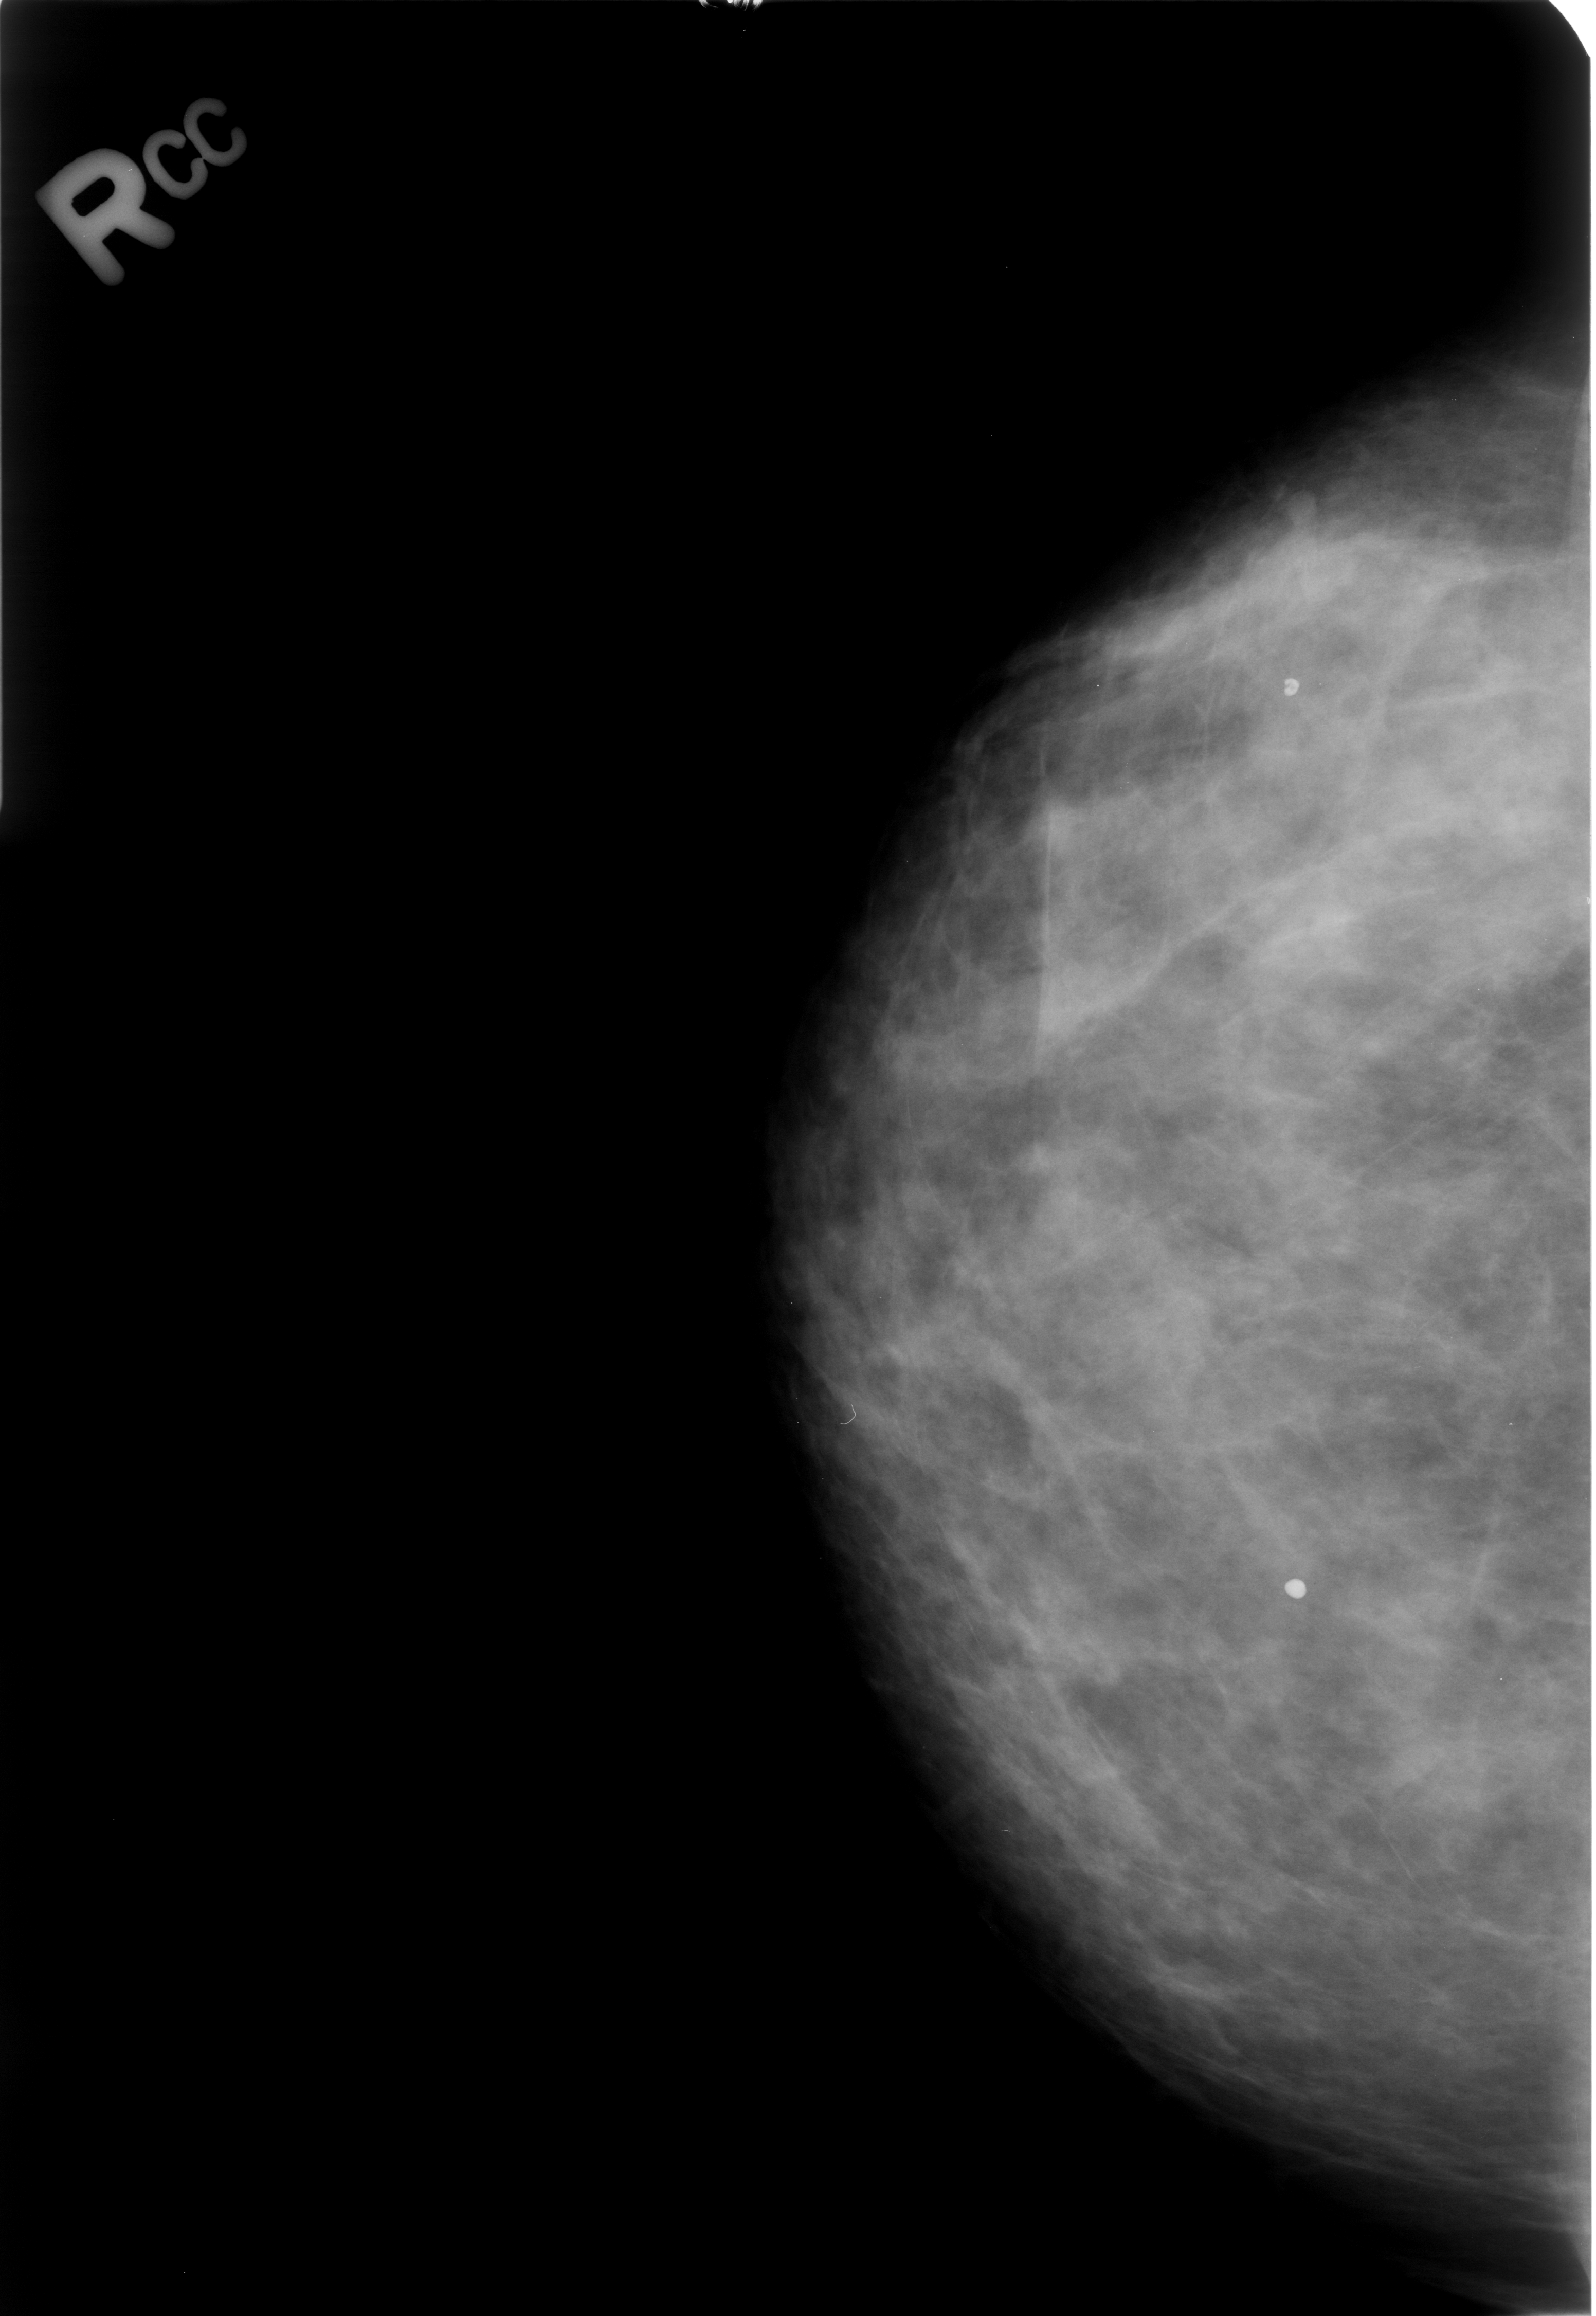
Scanned film-screen mammogram, right breast, CC view.
Marked findings (only marked abnormalities are described; nothing is implied about the rest of the image): Finding 1 of 2: calcifications, morphology coarse / round and regular / lucent centered; BI-RADS assessment category 2; subtlety rating 4 on a 1 (subtle) to 5 (obvious) scale; benign without callback (not worked up further). Finding 2 of 2: calcifications, morphology coarse / round and regular / lucent centered; BI-RADS assessment category 2; subtlety rating 4 on a 1 (subtle) to 5 (obvious) scale; benign; no additional work-up was recommended (benign without callback).